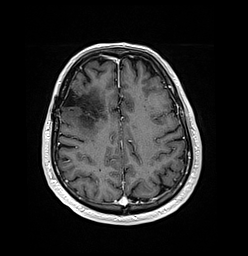
Brain MRI from a brain-tumour surgery series, one axial slice. Position 52 of 176 along the scan axis. T1-weighted post-contrast. 248 × 256 image matrix, field of view 242 × 250 mm. From the clinical record (not read from this slice): histopathology: Oligodendroglioma; WHO grade: 3; IDH mutation: yes.
Structures marked on this image (expert manual segmentation):
- previous resection cavity: bounding box <63,90,84,107> (left, top, right, bottom; pixels)